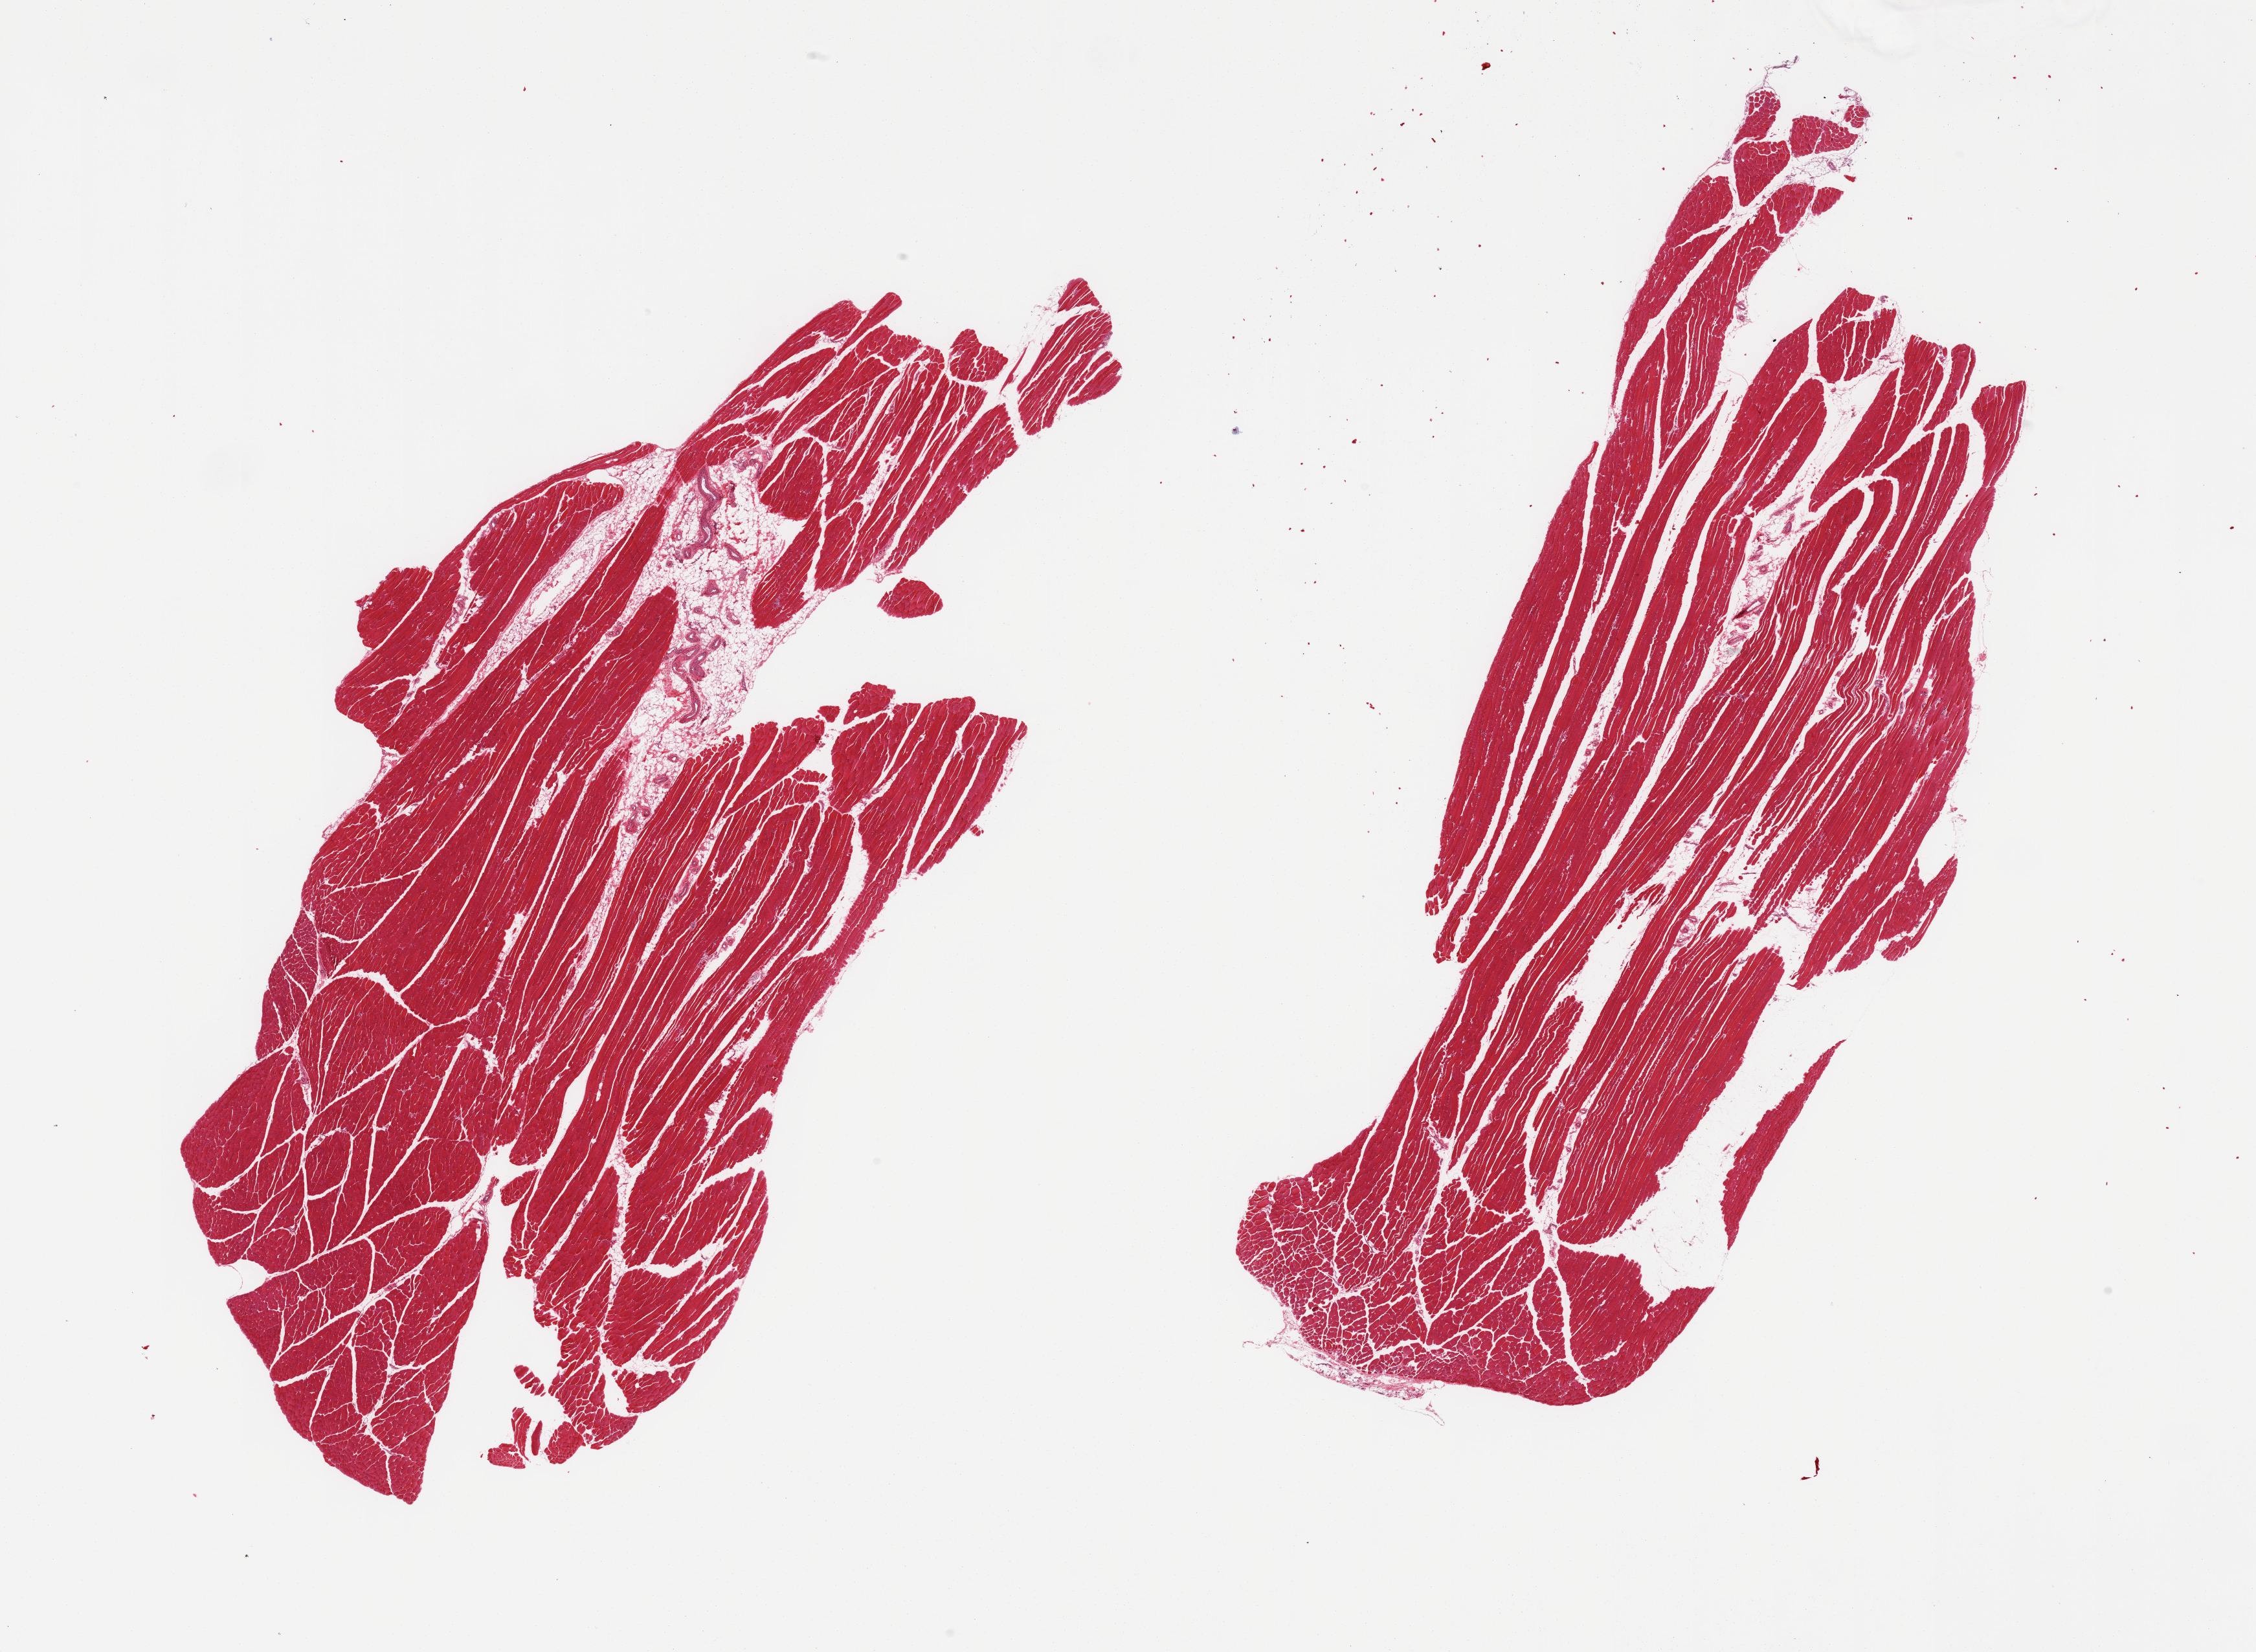
Digitized hematoxylin and eosin (H&E)-stained section, brightfield — shown as a low-resolution overview of the whole scanned area (about 27.6 x 20.2 mm, from a 20x scan). PAXgene-fixed, paraffin-embedded tissue. Target tissue: skeletal muscle. Donor tissue sample. Donor sex: female.
* pathologist's review note for this sample: 2 pieces; ~10 to 15% internal fat